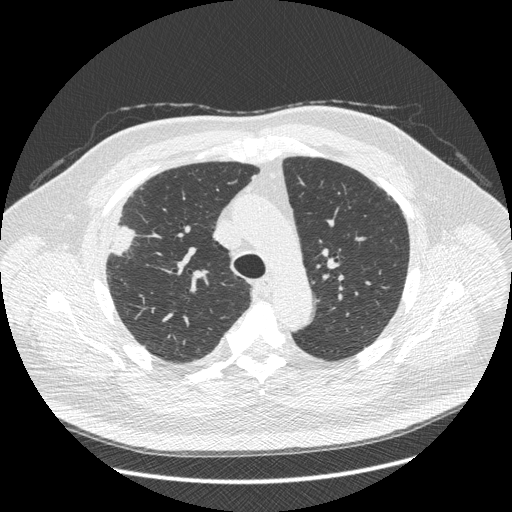
Low-dose screening chest CT, one axial slice. Position 307 of 426 along the scan axis. Reconstruction kernel STANDARD. Lung window (W 1500 / L -600 HU). 512 × 512 image matrix, field of view 400 × 400 mm.
Outlined on this slice (expert manual segmentation):
- lesion 1 (tumor, upper lobe of right lung): box from (x=110, y=226) to (x=135, y=255) px